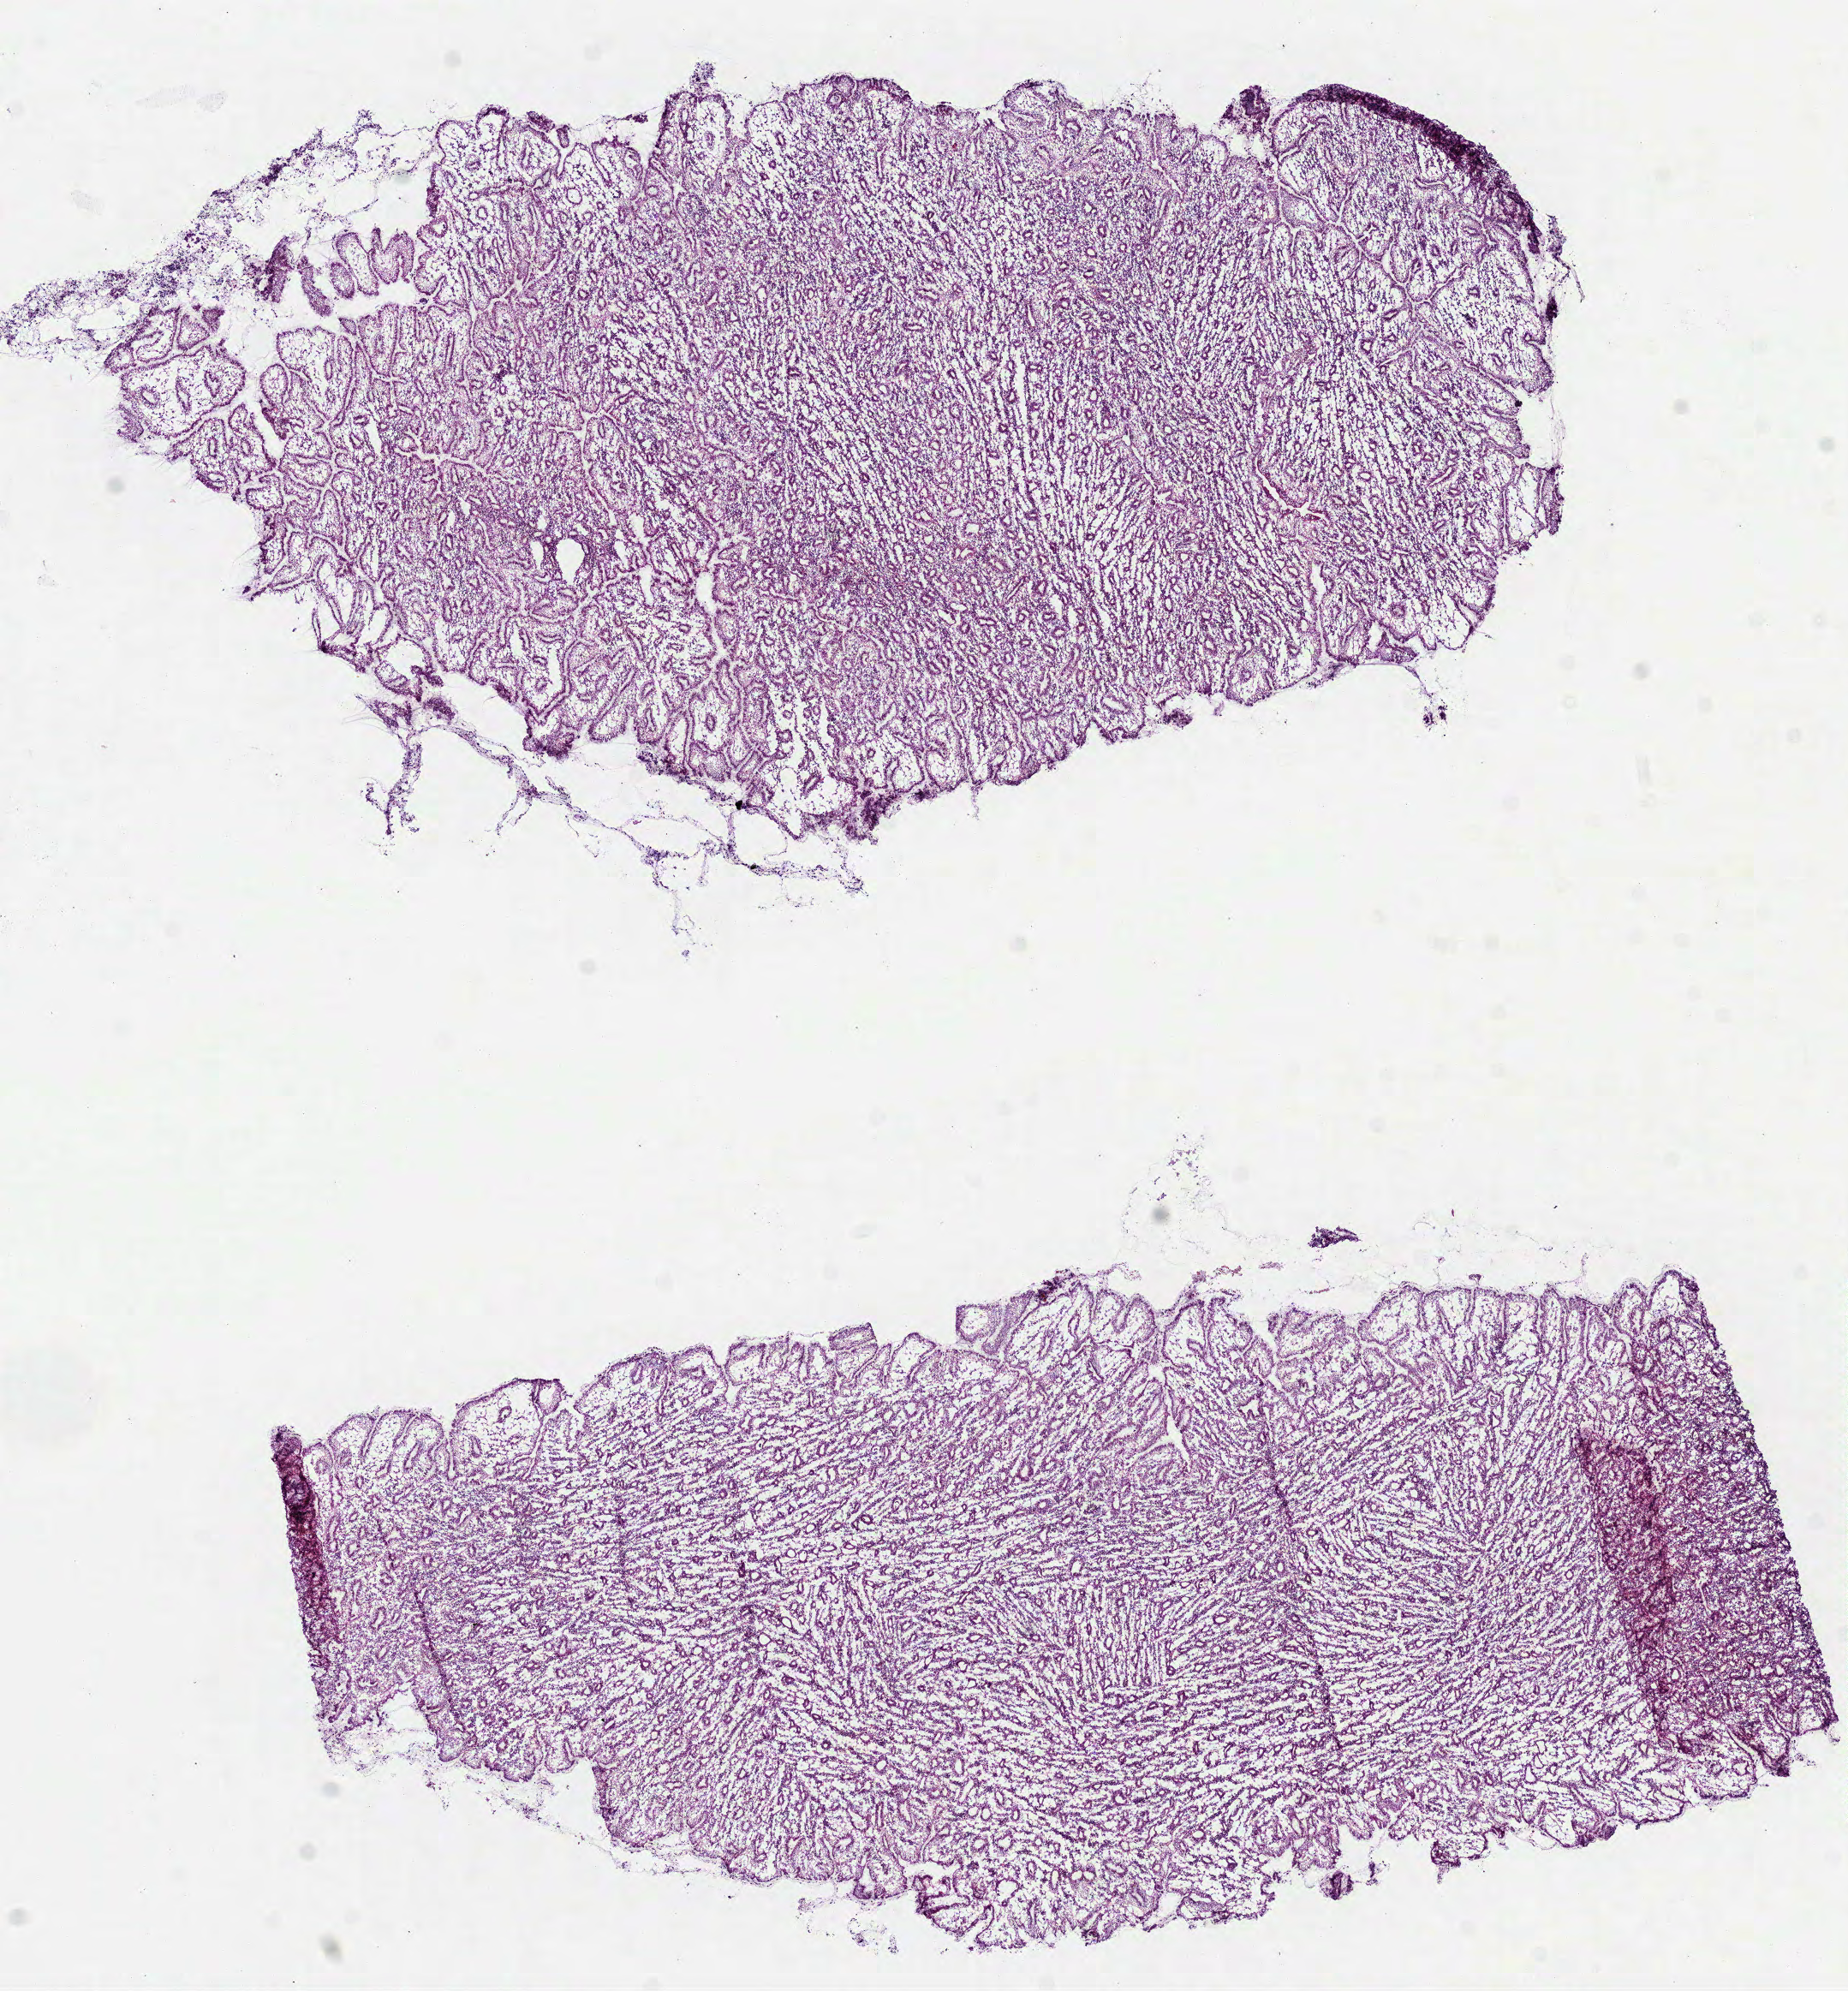
Hematoxylin and eosin (H&E) stained whole-slide image, a low-resolution overview of the entire scanned area, about 8.7 x 9.4 mm (from a 40x scan), frozen section from the top of the tissue portion, stomach, solid tissue normal (non-tumour tissue) sample. Patient: female, age at initial diagnosis 54 years.
This section: solid tissue normal sample (biorepository sample class). Patient diagnosis: Carcinoma, diffuse type.